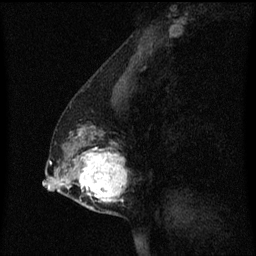
Breast MRI (dynamic contrast-enhanced), one sagittal slice; slice 26 of 60 in the series (ordered by position); dynamic contrast-enhanced series, image 2 of 3 at this slice position (ordered by acquisition); 1.5 T; TE 4.2 ms, TR 8.4 ms; 2 mm slice thickness; 256 × 256 image matrix, field of view 200 × 200 mm. Female patient, age 40 years. From the clinical record (not read from this slice): setting: breast cancer imaged before/during neoadjuvant chemotherapy; receptor status: triple-negative.
Annotated regions visible in this slice (semi-automatically segmented with operator editing):
- analysis volume of interest (the breast-tissue region the enhancement analysis was run in; not a lesion): bounding box <60,112,131,215> (left, top, right, bottom; pixels)
- tumour enhancement mask (voxels above the 70 % enhancement threshold inside the analysis volume of interest): <66,130,127,203>